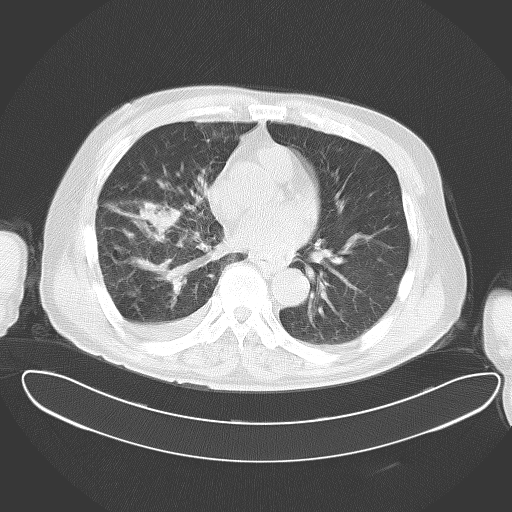
Chest CT, one axial slice. Slice 25 of 62 in the series (ordered by position). Reconstruction kernel B70f. Lung window (W 1500 / L -600 HU). 5 mm slice thickness. 512 × 512 image matrix, field of view 427 × 427 mm. Patient: male, 78 years. From the clinical record (not read from this slice): clinical TNM (as recorded): T2 N1 M1.
Annotated regions visible in this slice (rectangle marked by the reading radiologist):
- lung tumour (recorded histology: adenocarcinoma): box from (x=130, y=192) to (x=184, y=239) px